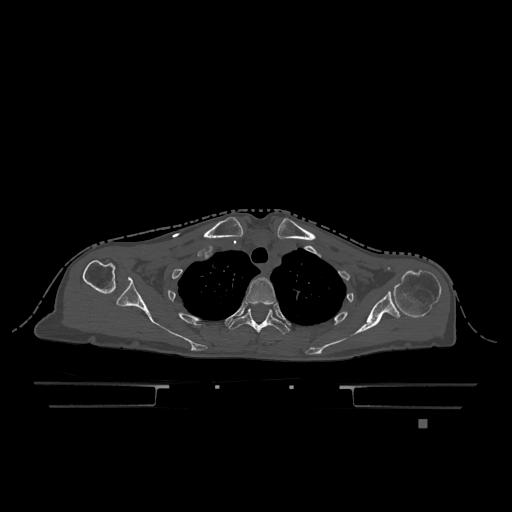
CT including the spine, one axial slice; slice 939 of 1317 in the series (ordered by position); bone window (W 1800 / L 400 HU); 0.5 mm slice thickness; 512 × 512 image matrix, field of view 500 × 500 mm. Patient: female, 74 years. Case-level facts recorded for this patient, not image findings: primary cancer: lung.
Annotated regions visible in this slice (semi-automatic segmentation, software-assisted and operator-edited):
- T2 vertebra: bounding box (x1, y1, x2, y2) in pixels: (244, 277, 276, 305)
- T3 vertebra: (229, 309, 290, 334)